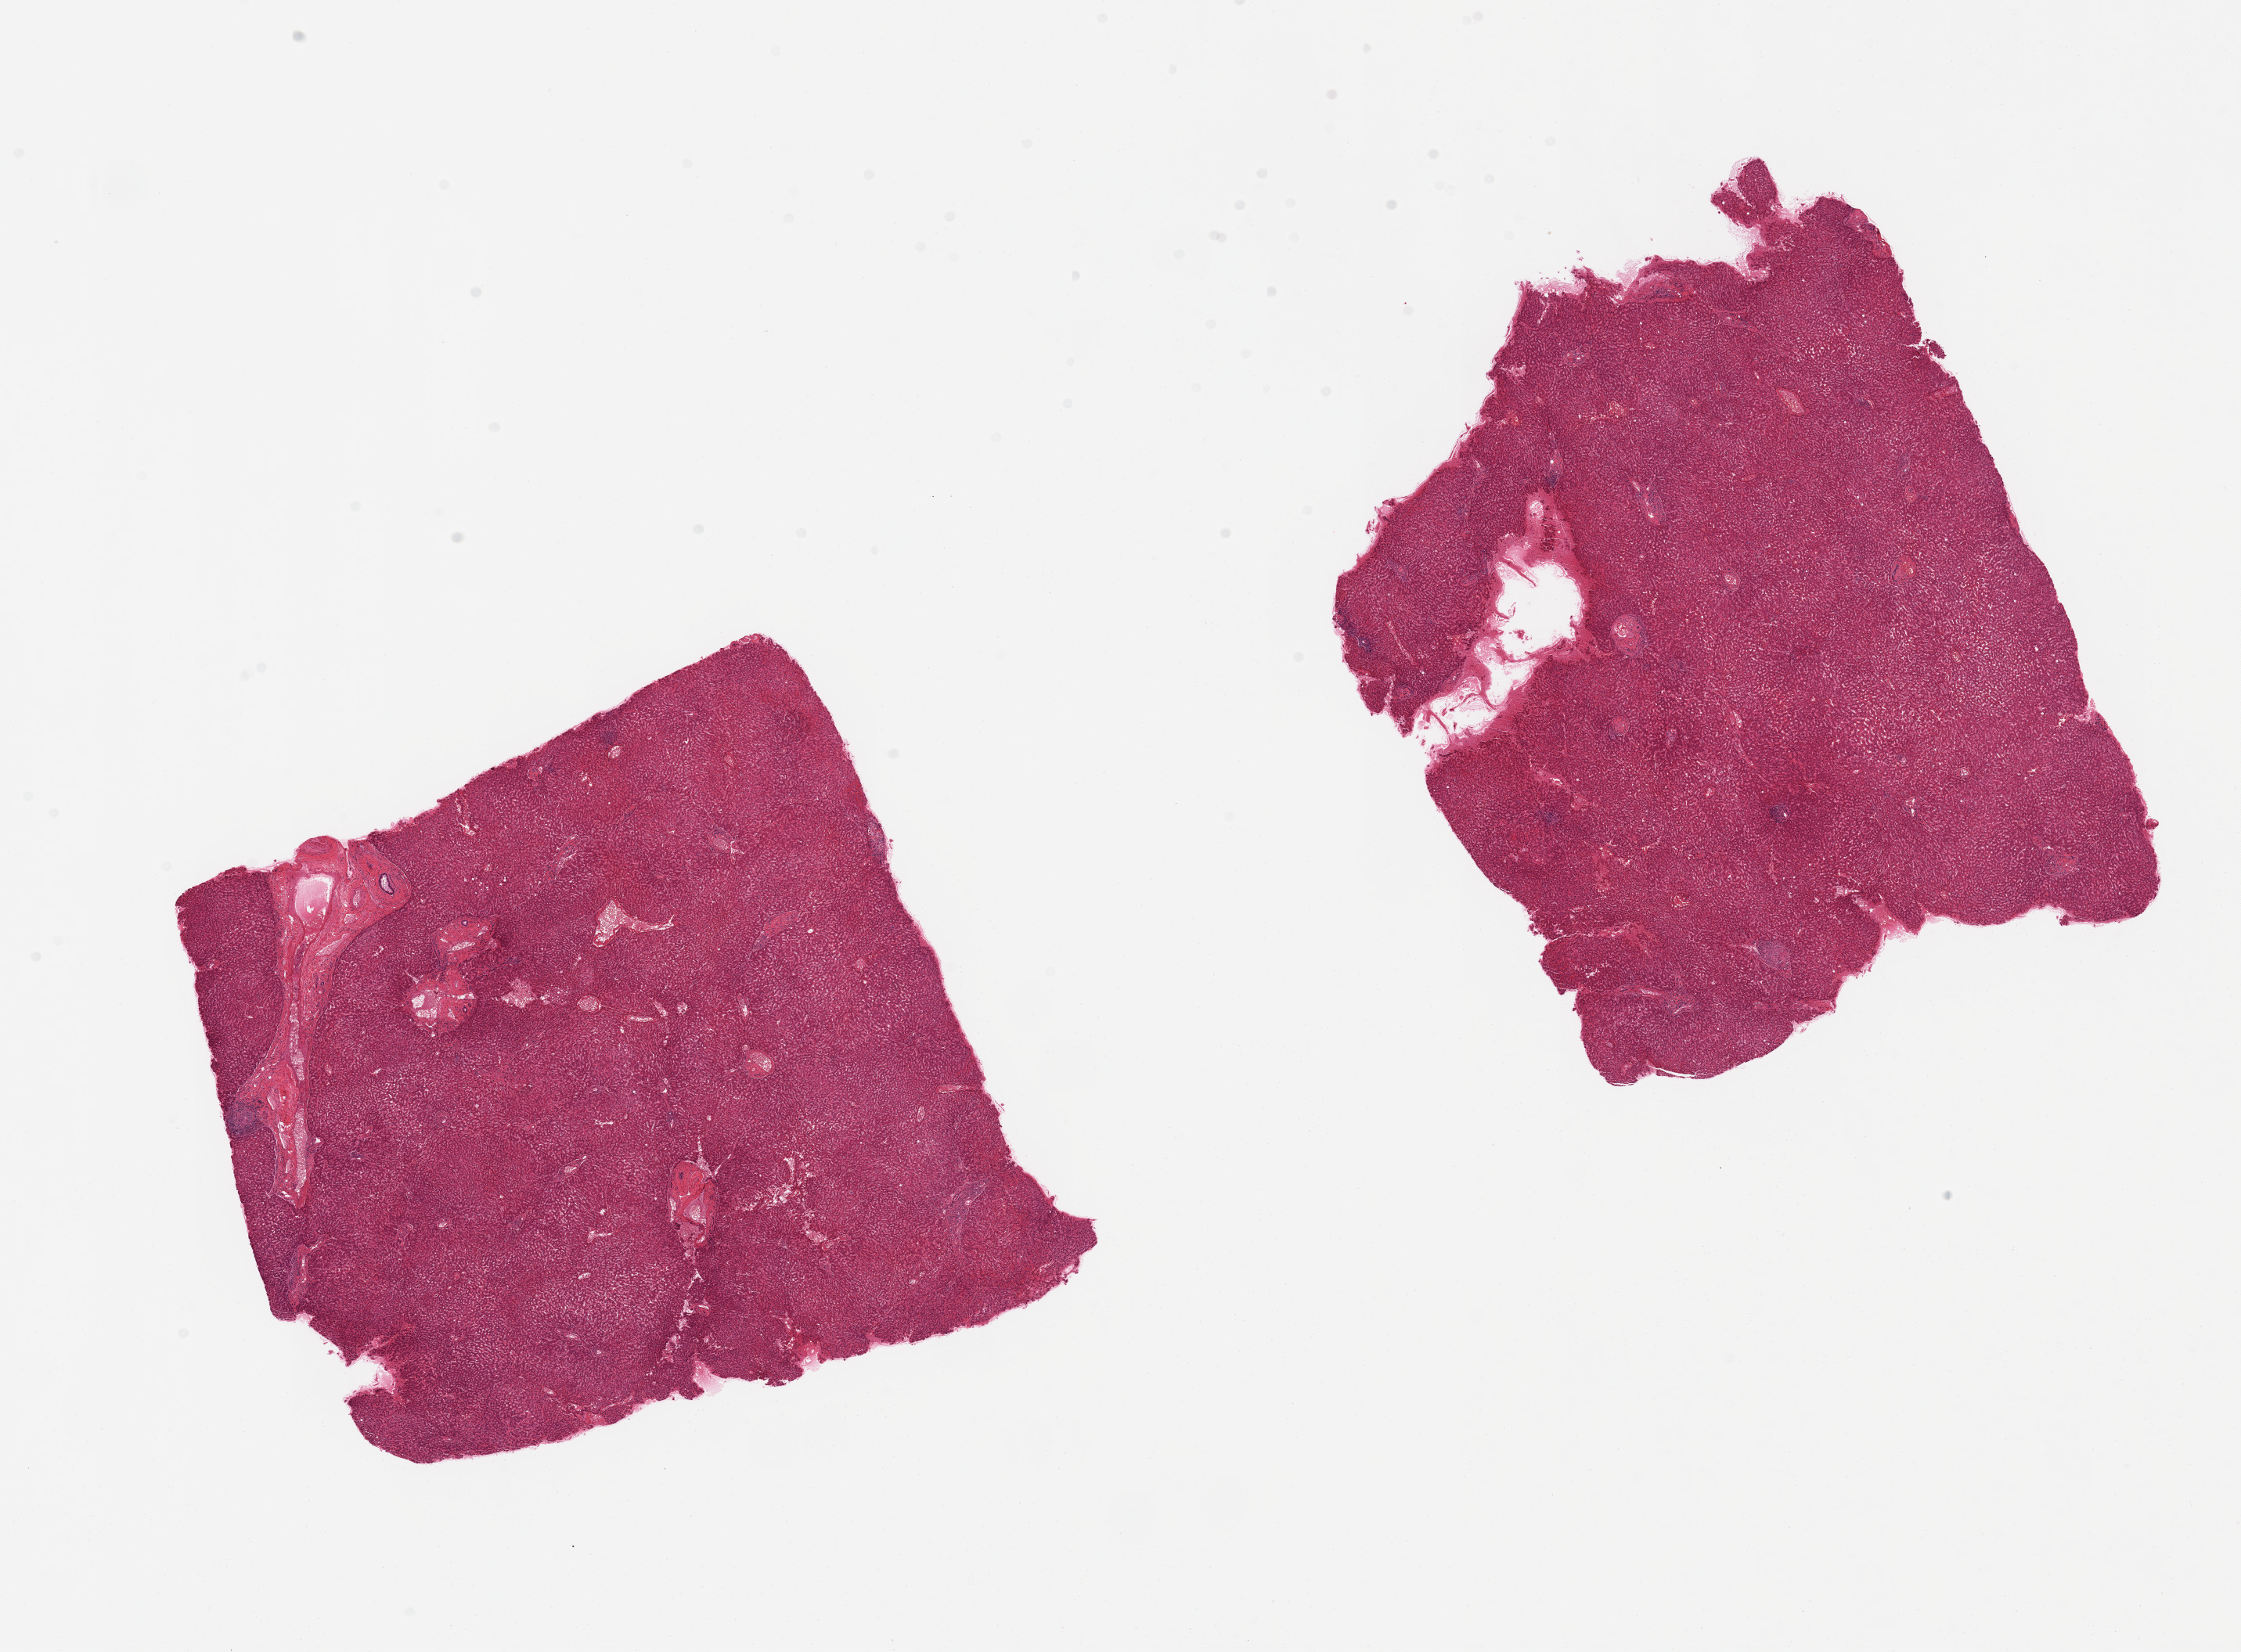
Digitized H&E-stained section, a low-resolution overview of the entire scanned area, about 22.6 x 16.7 mm. PAXgene-fixed paraffin-embedded (PFPE) section. Target tissue: liver. Donor tissue sample. Female donor.
Pathologist's review note for this sample: 2 pieces, no major abnormalities.